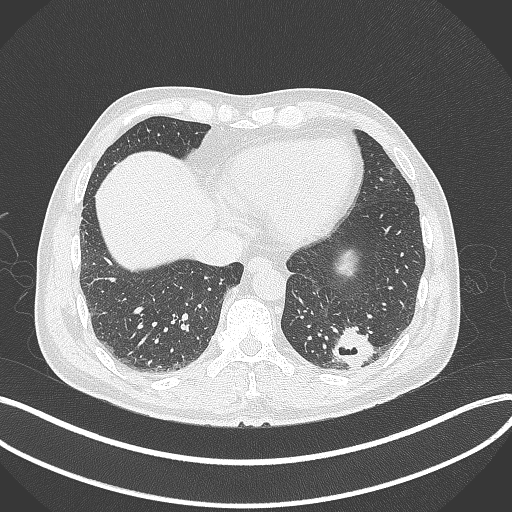
Chest CT, one axial slice; position 71 of 300 along the scan axis; 120 kVp; lung window (W 1500 / L -600 HU); 512 × 512 image matrix. Patient: male, 54 years. From the clinical record (not read from this slice): clinical TNM (as recorded): T1c N0 M1.
Annotated regions visible in this slice (rectangle marked by the reading radiologist):
- lung tumour (recorded histology: adenocarcinoma): bounding box [x1, y1, x2, y2] px = [329, 325, 377, 375]